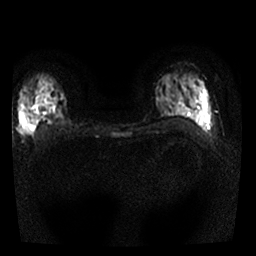
Breast MRI, one axial slice; position 16 of 25 along the scan axis; diffusion-weighted series; image 2 of 4 stored at this slice position (different b-values; order by instance number); 1.5 T; 4 mm slice thickness; 256 × 256 image matrix, field of view 300 × 300 mm. Female patient.
Outlined on this slice (expert manual segmentation):
- tumour on diffusion-weighted imaging: bounding box [x1, y1, x2, y2] px = [20, 109, 34, 132]